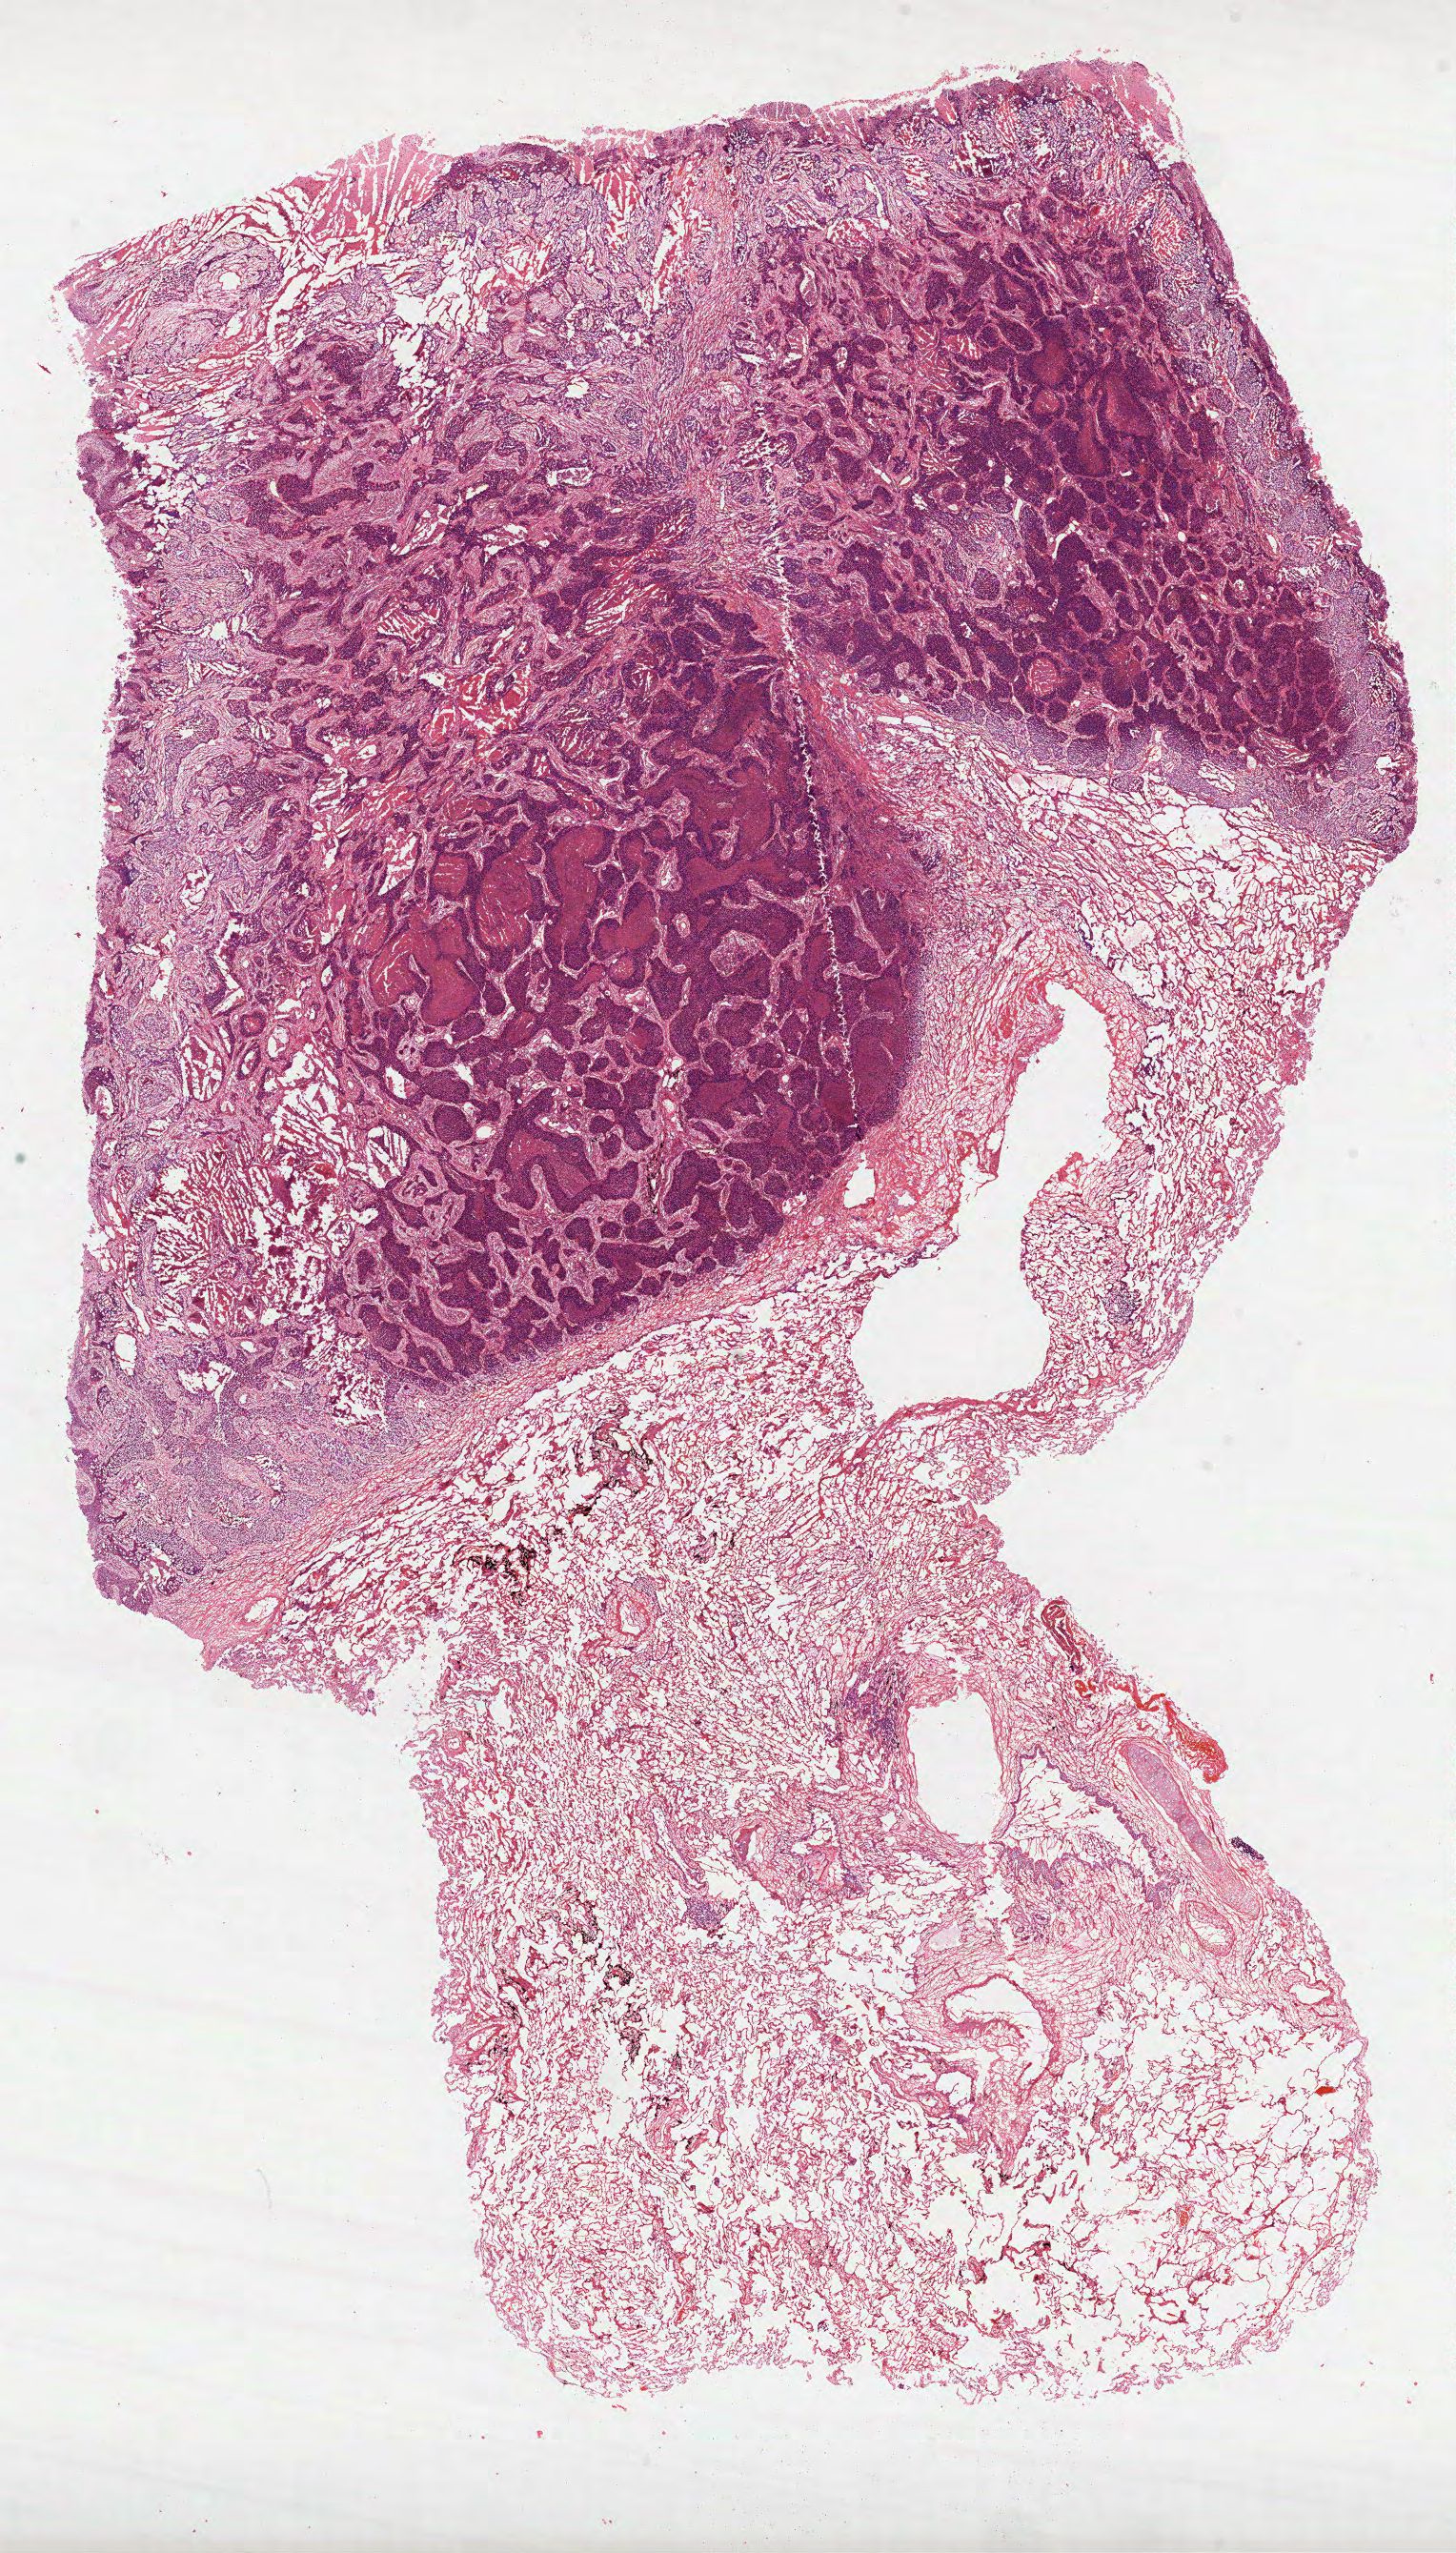
Hematoxylin and eosin (H&E) stained whole-slide image, shown as a low-resolution overview of the whole scanned area (about 12.3 x 21.6 mm, slide scanned at 40x); FFPE section; primary tumour sample from the lung. Male, age 73 years at initial diagnosis.
Histologic diagnosis: Squamous cell carcinoma, NOS. AJCC pathologic stage: IIB (7th edition). Laterality: right.